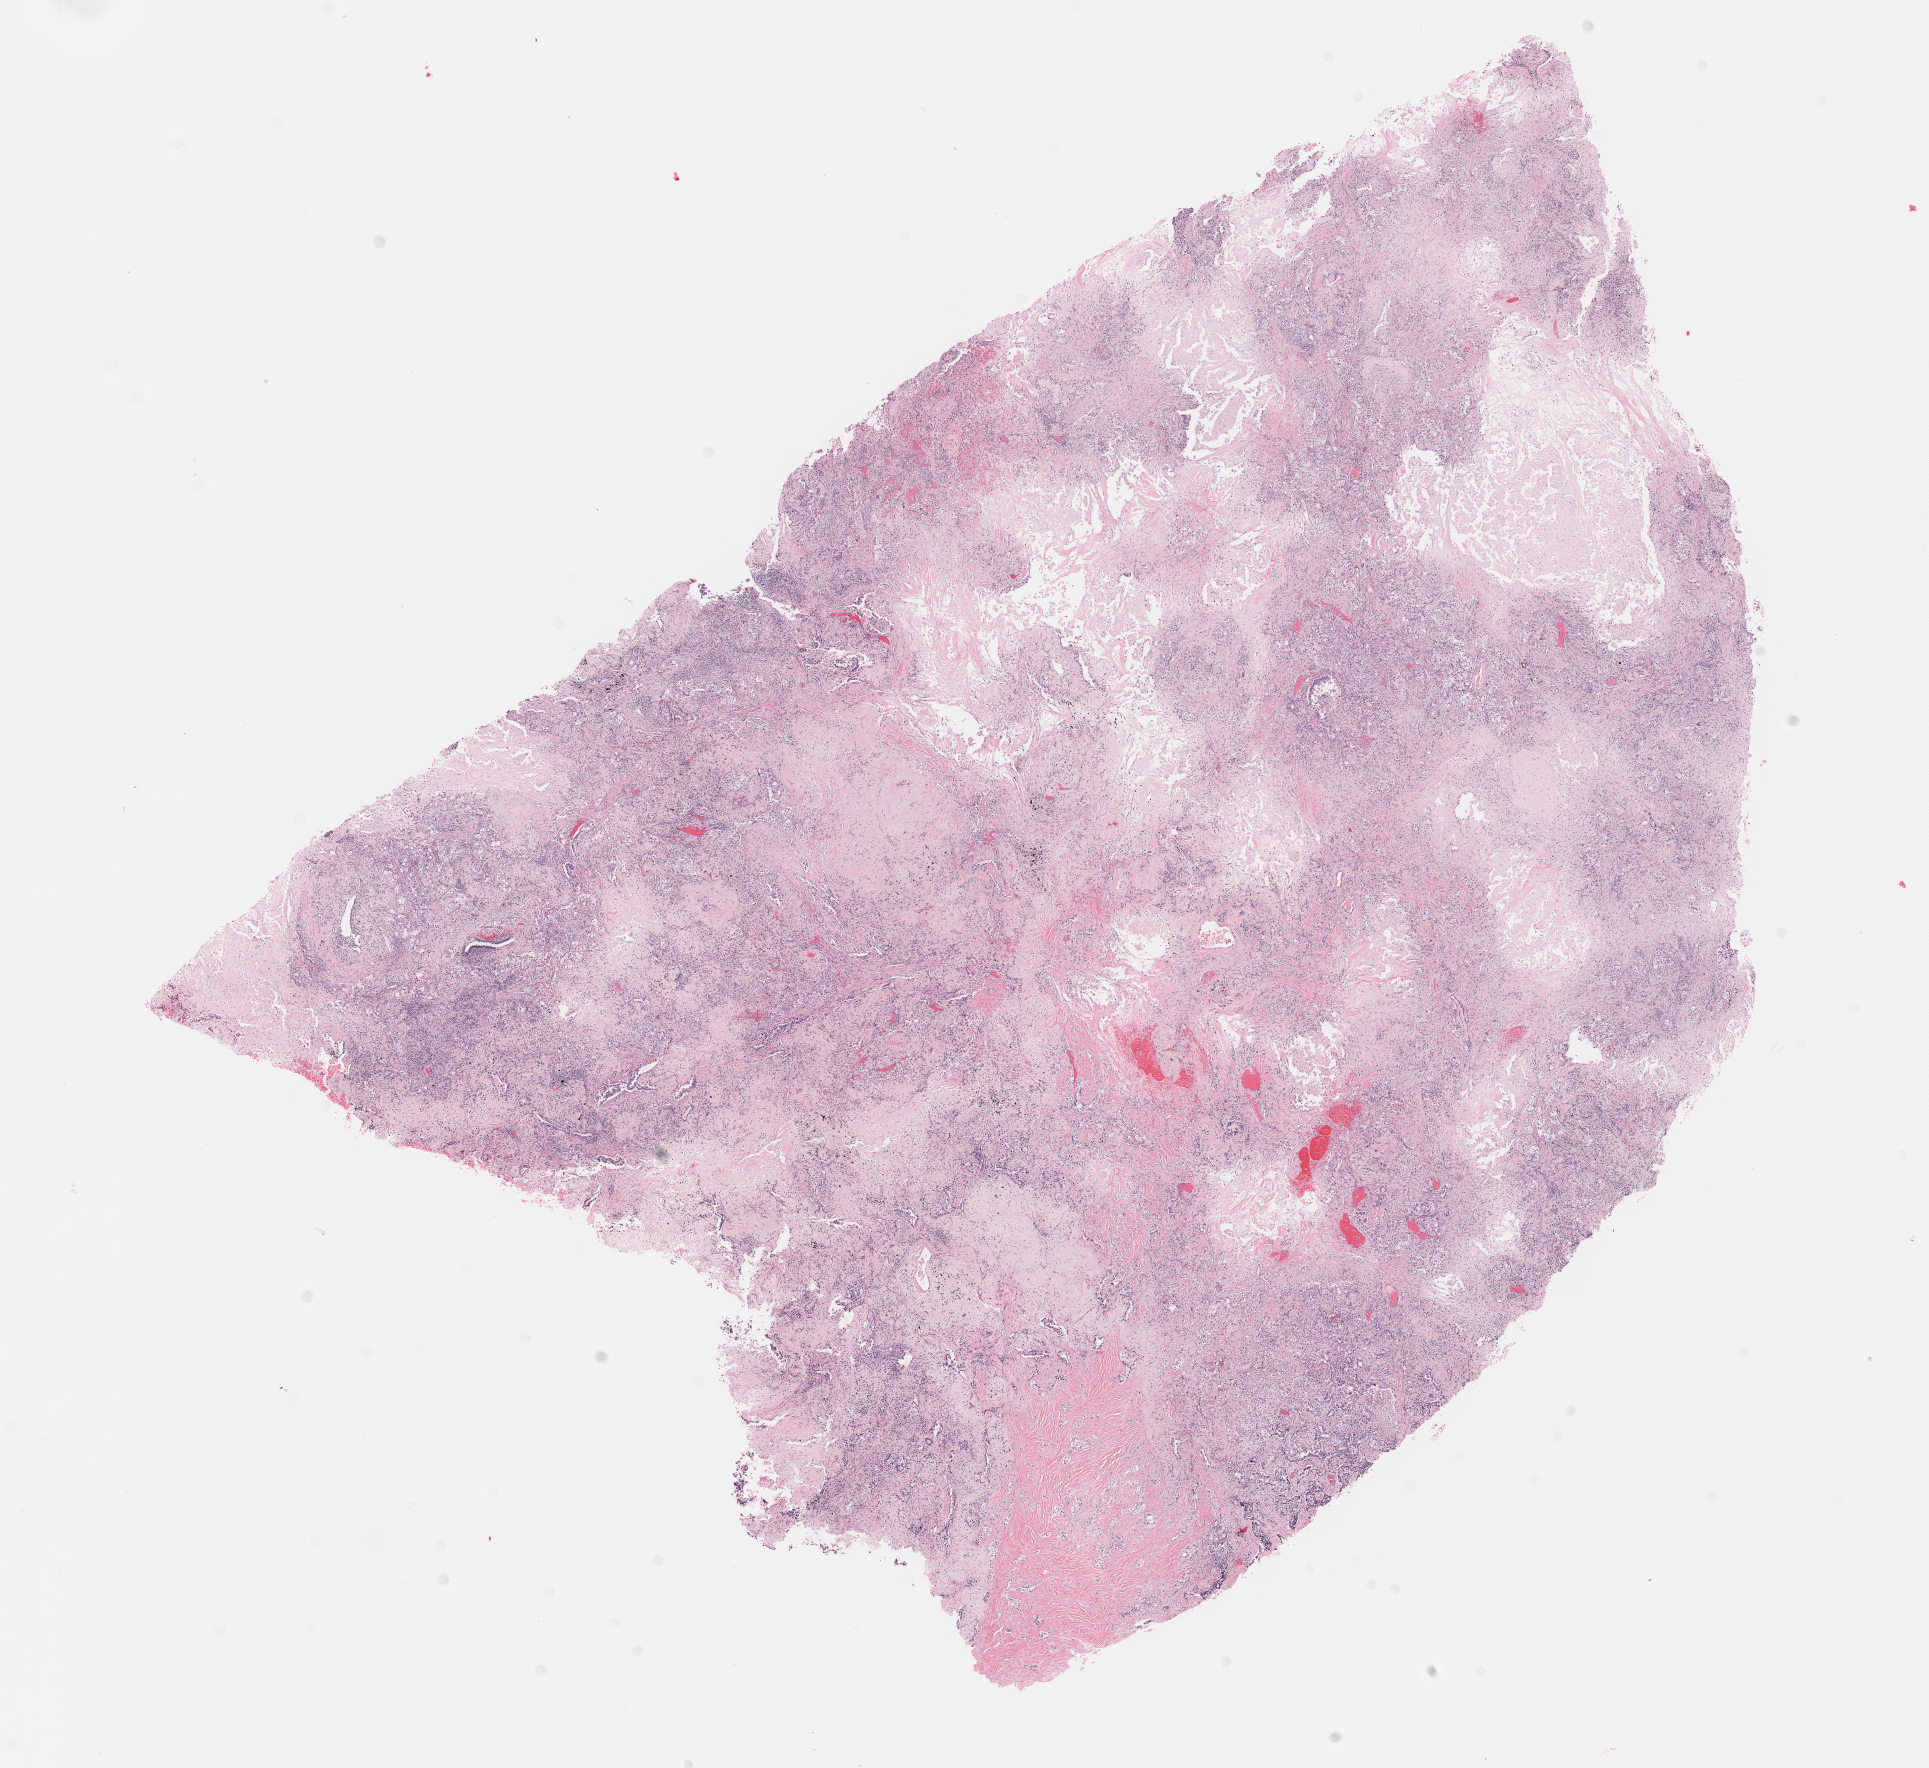
Whole-slide histology image, Hematoxylin and eosin (H&E) stained, shown as a low-resolution overview of the whole scanned area (about 15.6 x 14.3 mm), FFPE section, sample: primary tumour, lung. Male patient; age at initial diagnosis 74 years.
Pathologic diagnosis: Adenocarcinoma with mixed subtypes (upper lobe, lung).